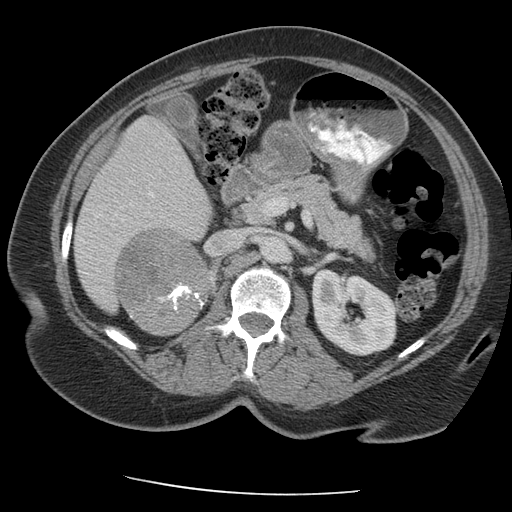
Contrast-enhanced abdominal CT, one axial slice; position 116 of 163 along the scan axis; reconstruction kernel STANDARD; 140 kVp; intravenous contrast given; soft-tissue window (W 400 / L 40 HU); 512 × 512 image matrix, field of view 360 × 360 mm. Patient: female, 70 years. Case-level facts recorded for this patient, not image findings: diagnosis: adrenocortical carcinoma; tumour side: right adrenal; tumour size at pathology: 9.5 cm; Ki-67 index: 5 %; stage (as recorded): 2.
Outlined on this slice (semi-automatic segmentation, software-assisted and operator-edited):
- mass: bounding box <117,230,210,335> (left, top, right, bottom; pixels)